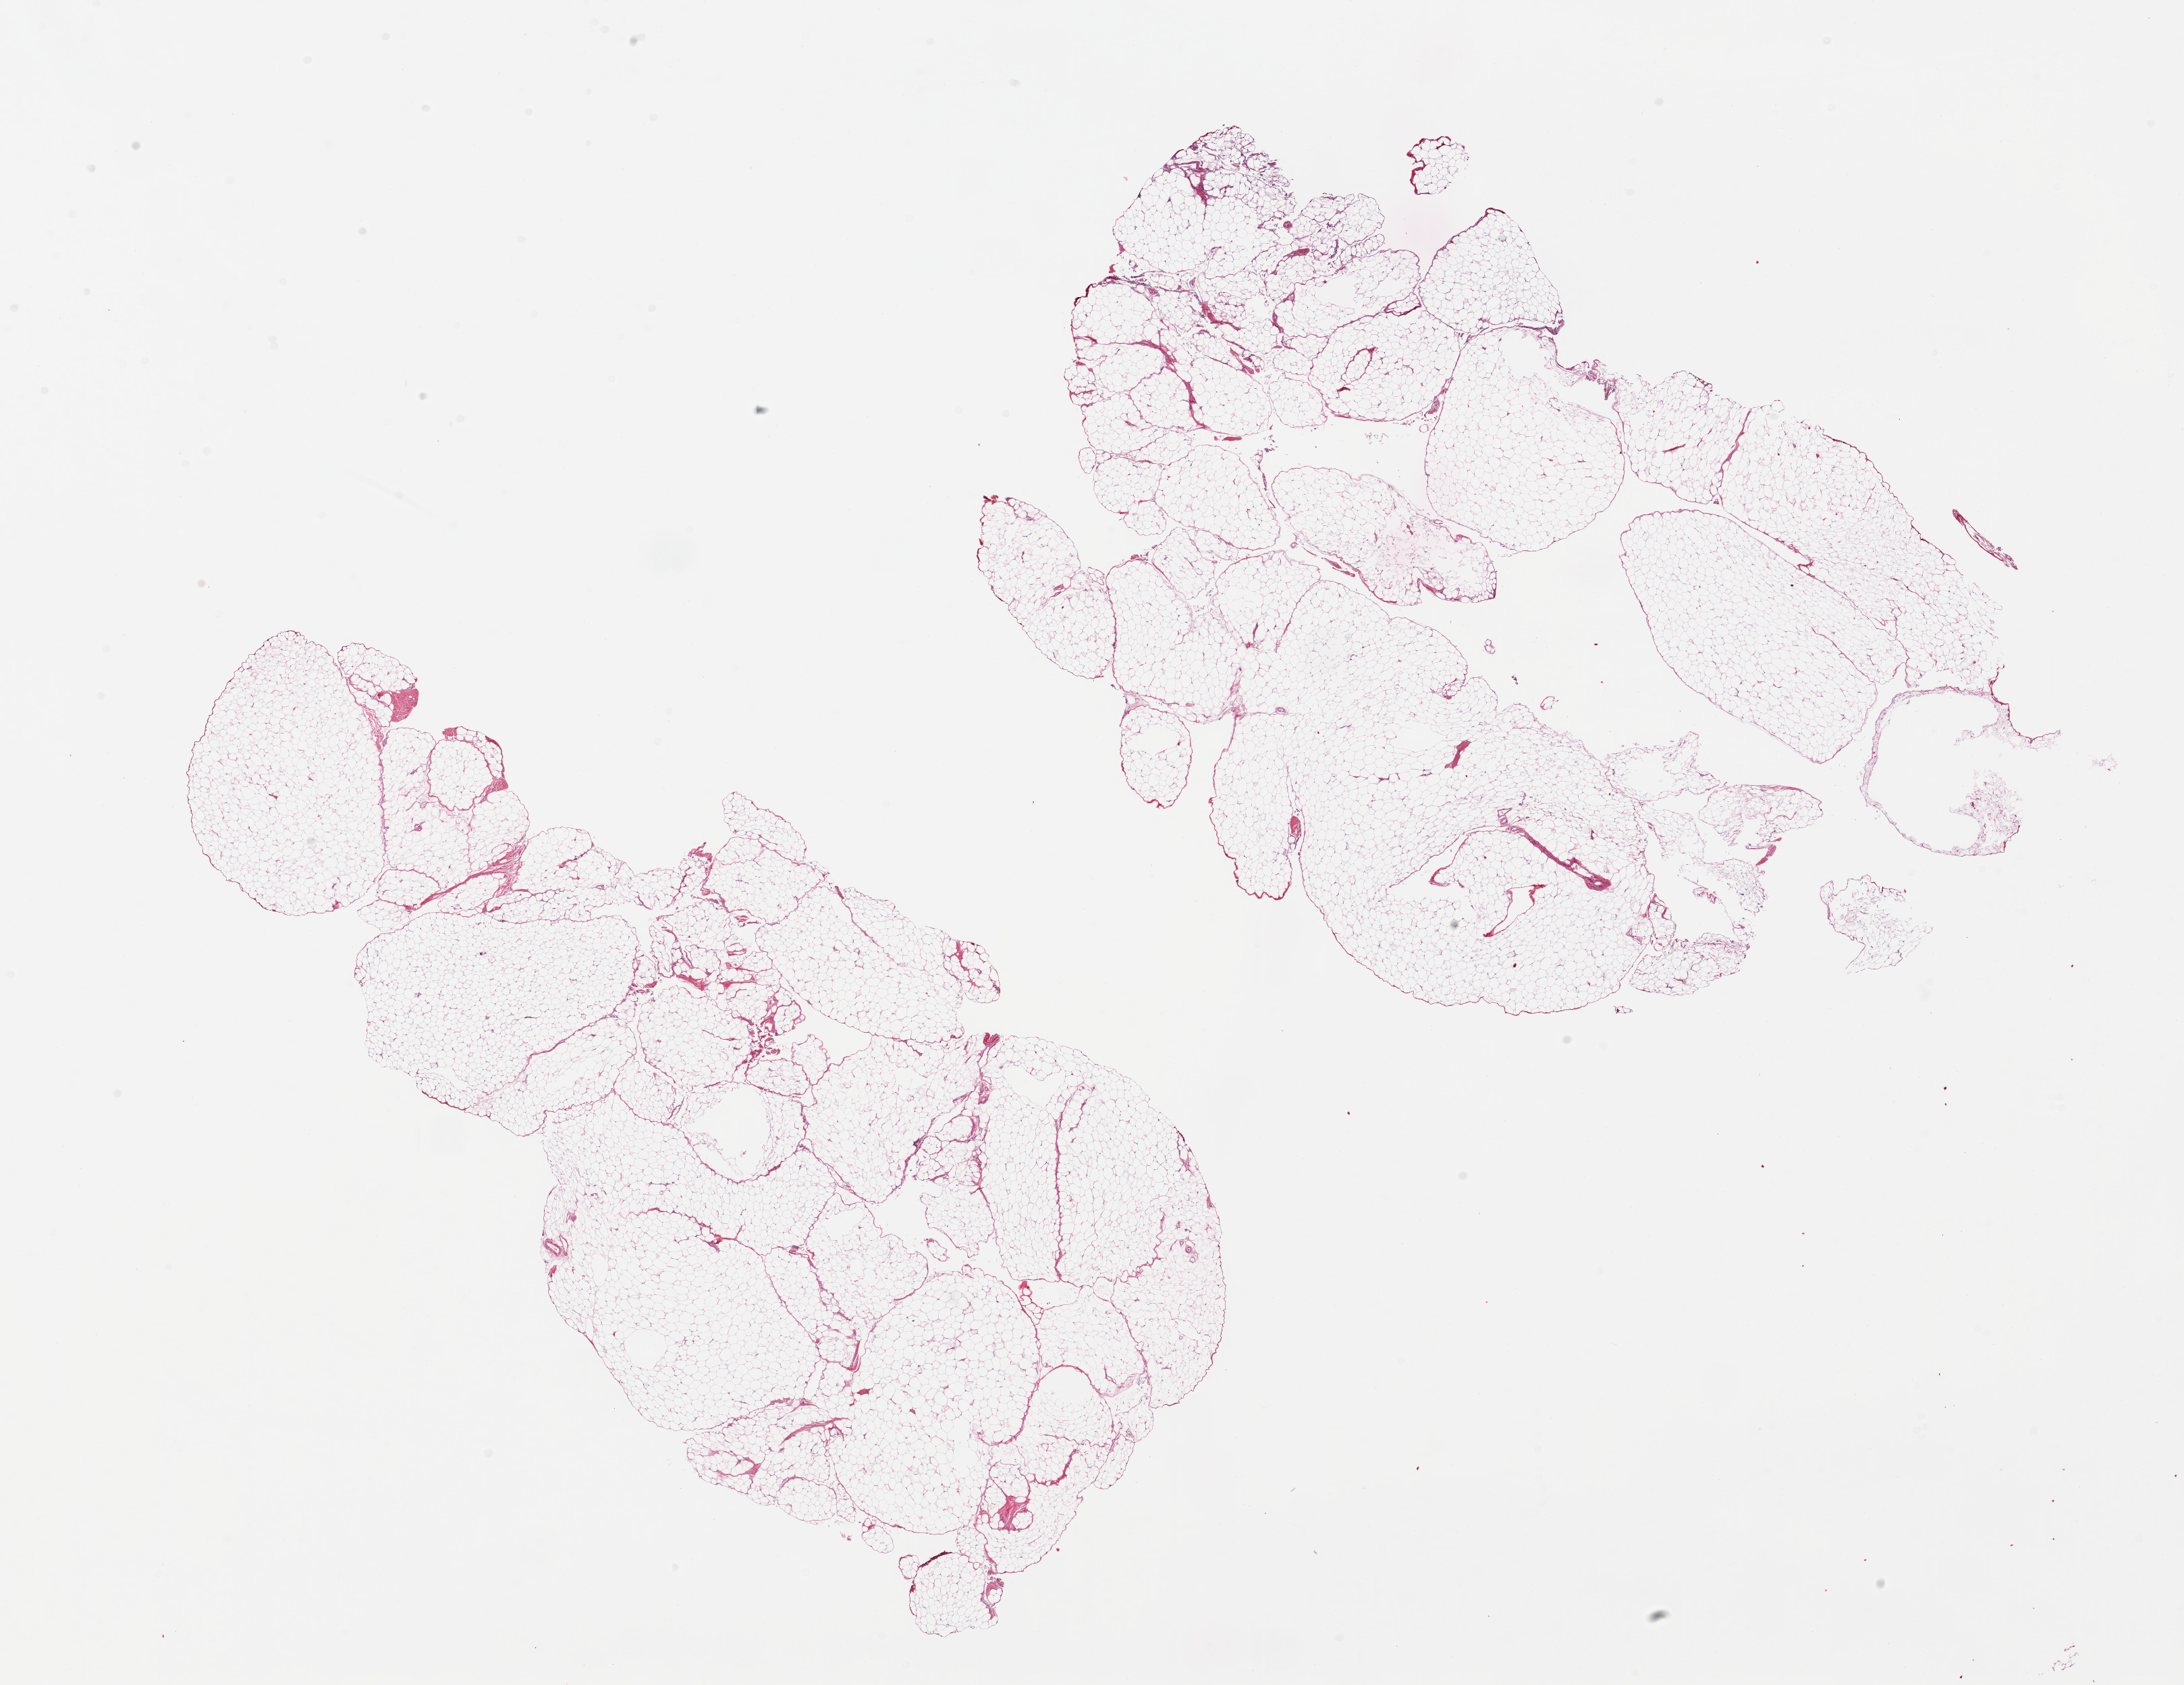
Haematoxylin and eosin whole-slide image — whole scanned area (about 25.6 x 19.7 mm) shown as a low-resolution overview; PAXgene-fixed paraffin-embedded (PFPE) section; section of omentum (target tissue); donor tissue sample. Male donor.
Pathologist's review note for this sample: 2 pieces; minimal fibrous content.